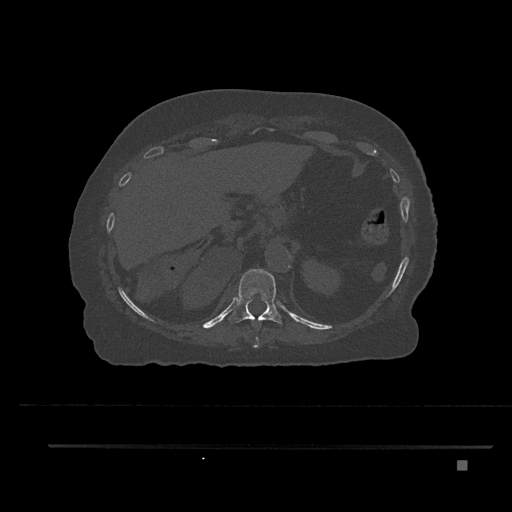
CT including the spine, one axial slice; 120 kVp; bone window (W 1800 / L 400 HU); 0.5 mm slice thickness; 512 × 512 image matrix, field of view 437 × 437 mm. Female patient, age 76 years. Case-level facts recorded for this patient, not image findings: primary cancer: lung; vertebrae with lytic lesions (as recorded): T11, L3.
Annotated regions visible in this slice (semi-automatic segmentation, software-assisted and operator-edited):
- T10 vertebra: bounding box <253,336,259,348> (left, top, right, bottom; pixels)
- T11 vertebra: <229,269,283,325>